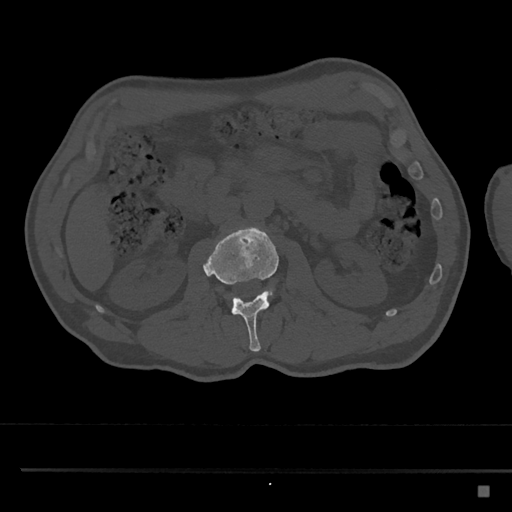
CT including the spine, one axial slice. Slice 747 of 797 in the series (ordered by position). Reconstruction kernel Br40s/3. 120 kVp. Bone window (W 1800 / L 400 HU). 0.5 mm slice thickness. 512 × 512 image matrix, field of view 391 × 391 mm. Patient: male, 59 years. Case-level facts recorded for this patient, not image findings: primary cancer: prostate.
Outlined on this slice (semi-automatically segmented with operator editing):
- L2 vertebra: bounding box (x1, y1, x2, y2) in pixels: (203, 226, 280, 352)